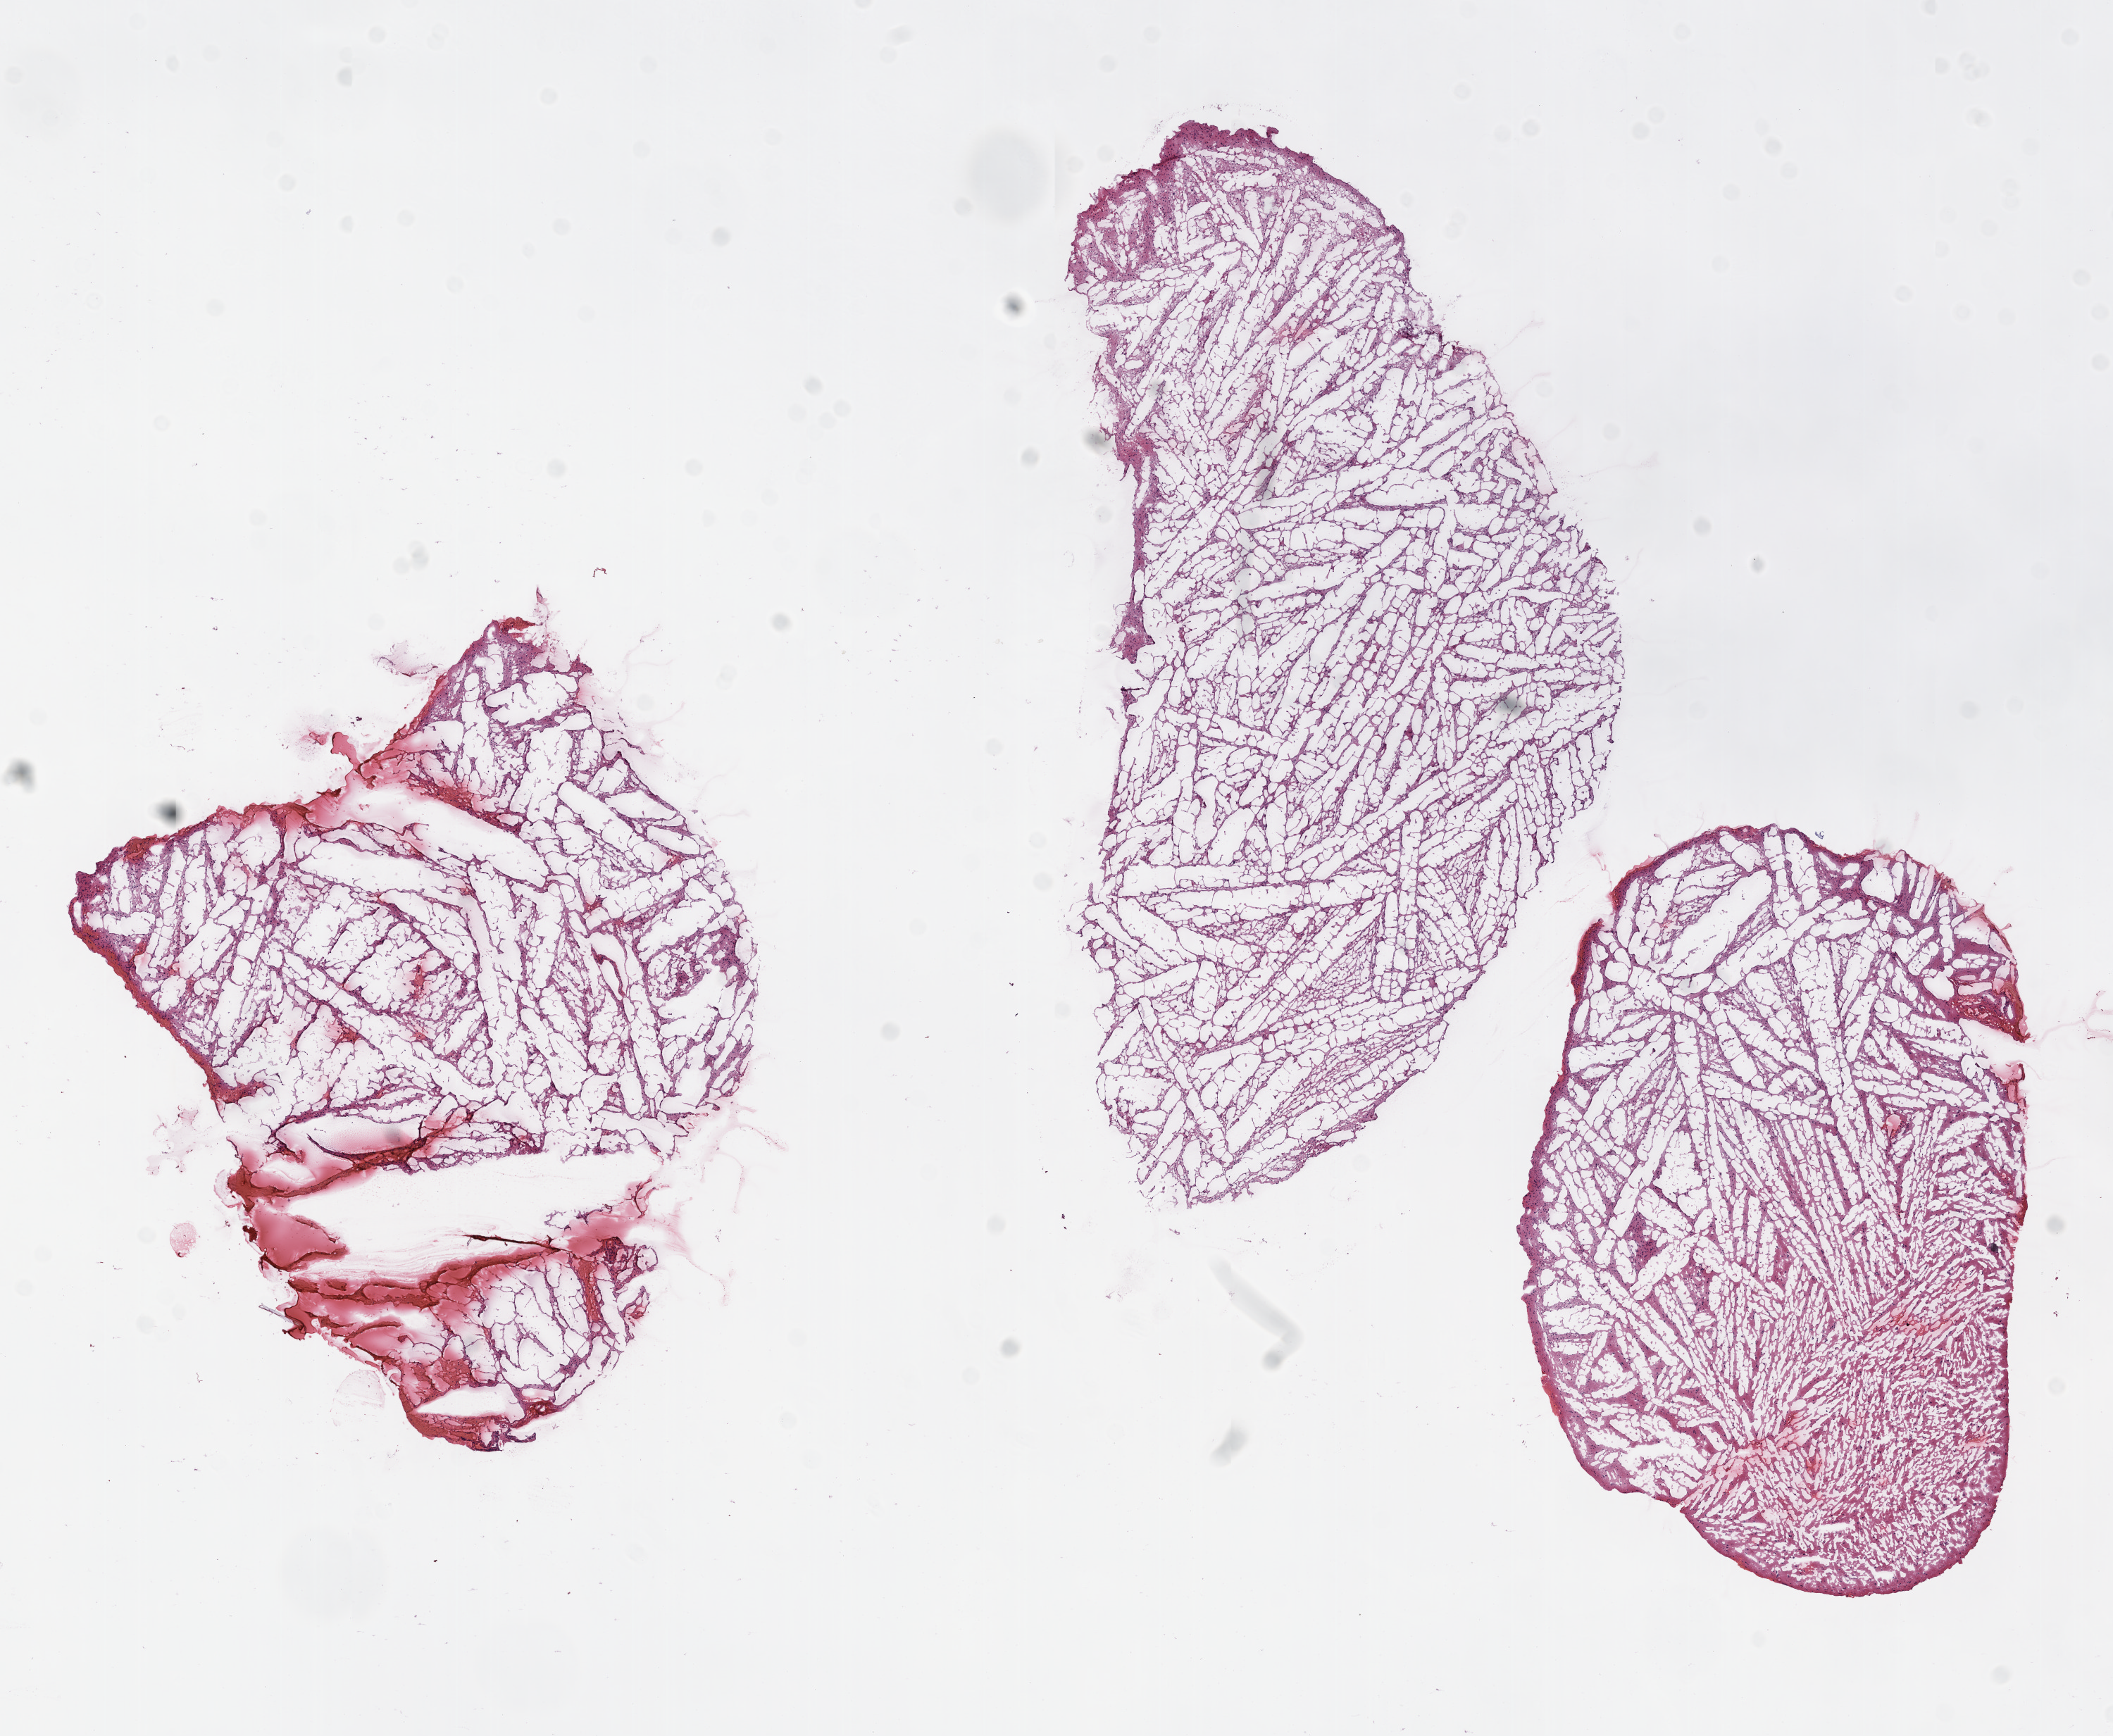
H&E whole-slide image — low-resolution overview of the scanned area, about 12.0 x 9.9 mm. Frozen section from the top of the tissue portion. Brain, primary tumour sample. Patient: female, age at initial diagnosis 44 years. Histologic grade: G3 (poorly differentiated). Pathologist review of this section (percent, as recorded): tumour cells 100%, tumour nuclei 60%, normal cells 0%, stromal cells 0%, necrosis 0%.
Diagnosis: Astrocytoma, anaplastic. Laterality: right.